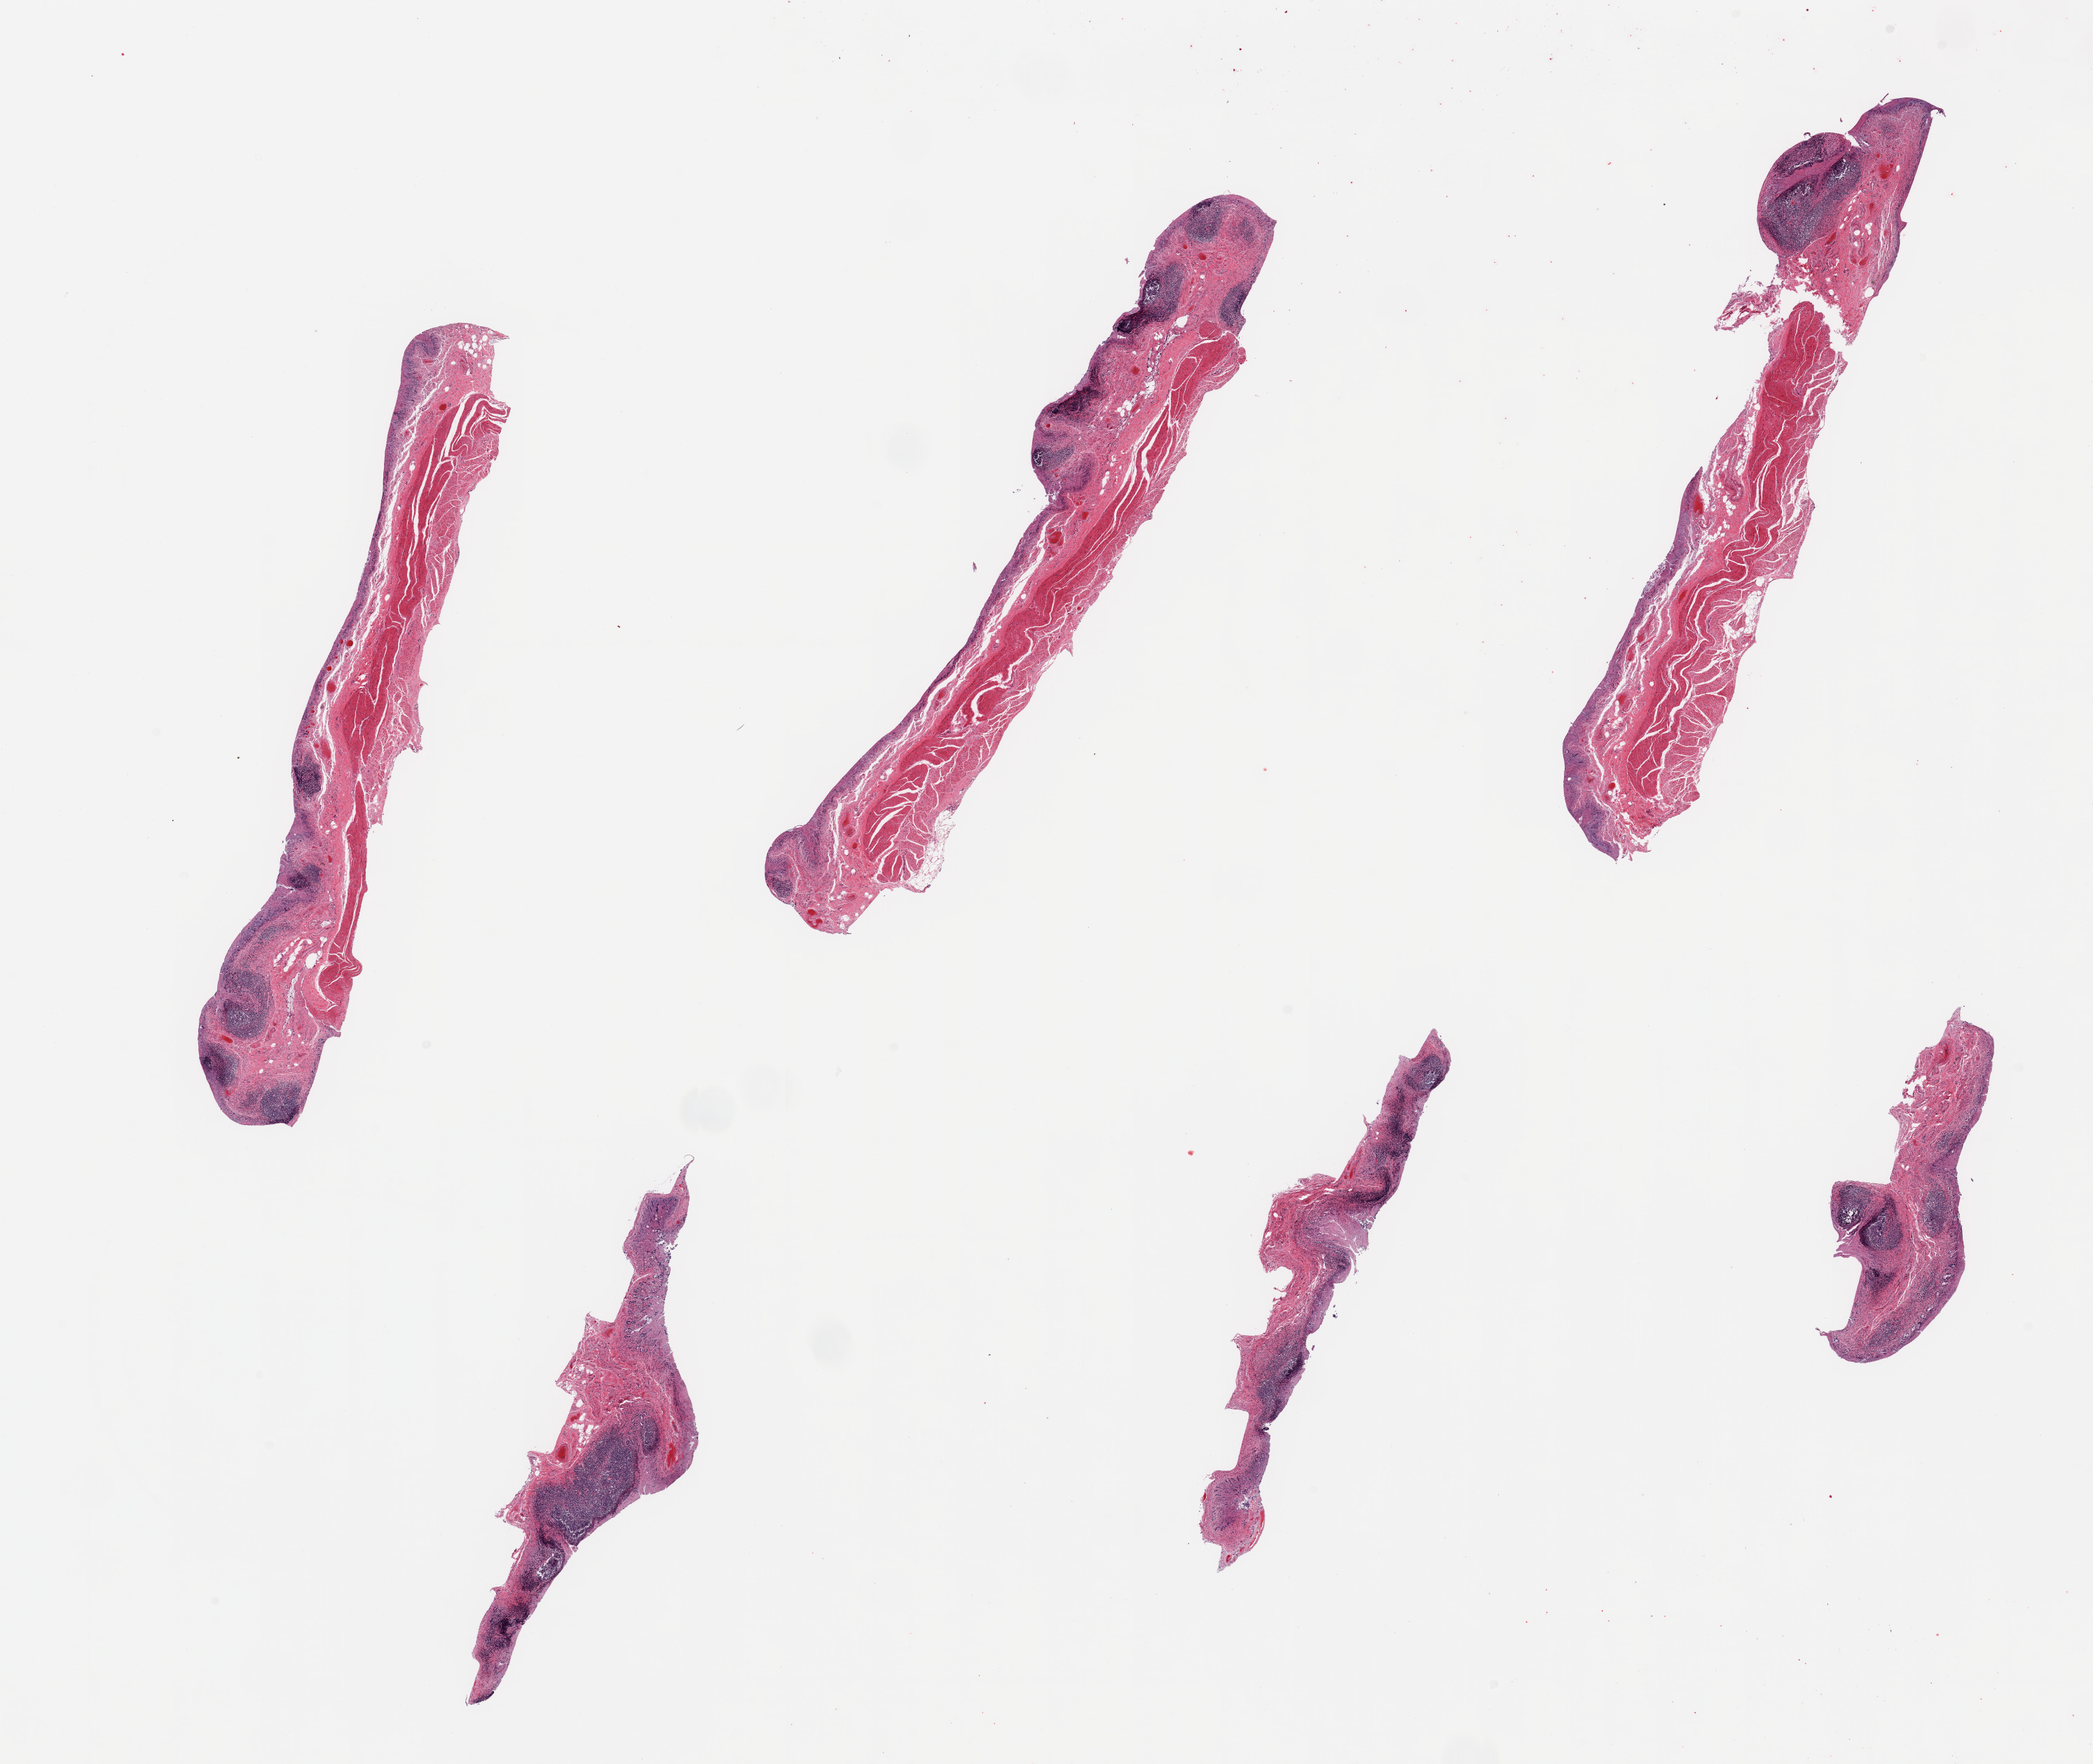
Whole-slide image, haematoxylin and eosin stain, brightfield — low-resolution overview of the scanned area, about 23.6 x 19.9 mm, PAXgene-fixed paraffin-embedded (PFPE) section, section of ileum (target tissue), tissue donor sample. Donor: male.
• review note (as recorded): 6 pieces, glandular elements with advanced autolysis but lymphoid aggregates are ~25-30% of tissue